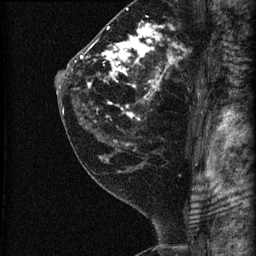
Breast MRI (dynamic contrast-enhanced), one sagittal slice. Slice 41 of 60 in the series (ordered by position). Dynamic contrast-enhanced series, image 2 of 3 at this slice position (ordered by acquisition). 1.5 T. TE 4.2 ms, TR 22.7 ms. 1.8 mm slice thickness. 256 × 256 image matrix, field of view 180 × 180 mm. Female patient, age 45 years. From the clinical record (not read from this slice): setting: breast cancer imaged before/during neoadjuvant chemotherapy; receptor status: HR-positive, HER2-negative.
Structures marked on this image (semi-automatic segmentation, software-assisted and operator-edited):
- analysis volume of interest (the breast-tissue region the enhancement analysis was run in; not a lesion): bounding box [x1, y1, x2, y2] px = [74, 11, 205, 140]
- tumour enhancement mask (voxels above the 90 % enhancement threshold inside the analysis volume of interest): [75, 20, 178, 117]